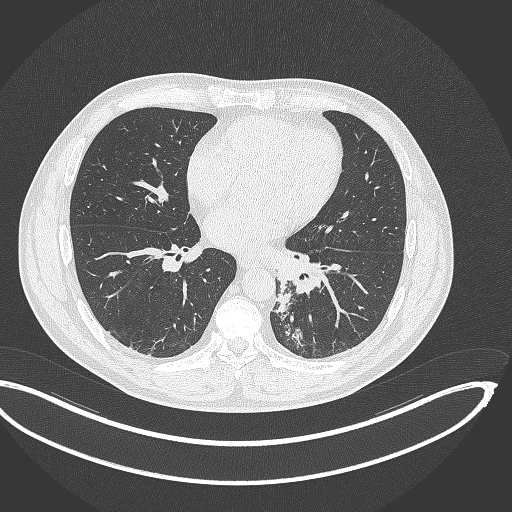
Chest CT, one axial slice; reconstruction kernel B70f; lung window (W 1500 / L -600 HU); 1 mm slice thickness; 512 × 512 image matrix, field of view 442 × 442 mm. Patient: male, 50 years. From the clinical record (not read from this slice): clinical TNM (as recorded): T2a N3 M0.
Structures marked on this image (rectangle marked by the reading radiologist):
- lung tumour (recorded histology: squamous cell carcinoma): box from (x=271, y=279) to (x=293, y=314) px